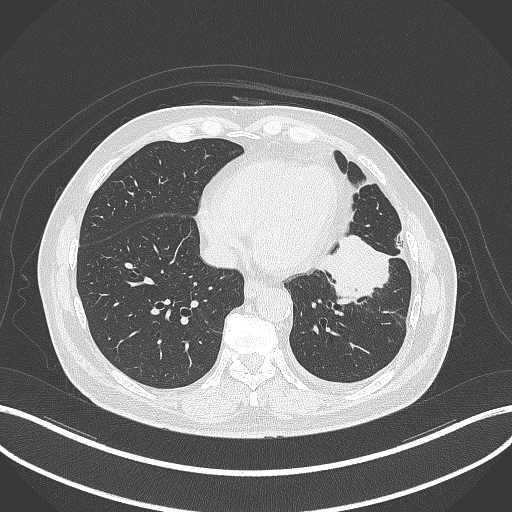
Chest CT, one axial slice; reconstruction kernel B70f; 120 kVp; lung window (W 1500 / L -600 HU); 1 mm slice thickness; 512 × 512 image matrix, field of view 400 × 400 mm. Patient: male, 68 years. From the clinical record (not read from this slice): clinical TNM (as recorded): T2b N0 M0.
Structures marked on this image (bounding box drawn by a radiologist):
- lung tumour (recorded histology: squamous cell carcinoma): bounding box [x1, y1, x2, y2] px = [315, 229, 394, 311]